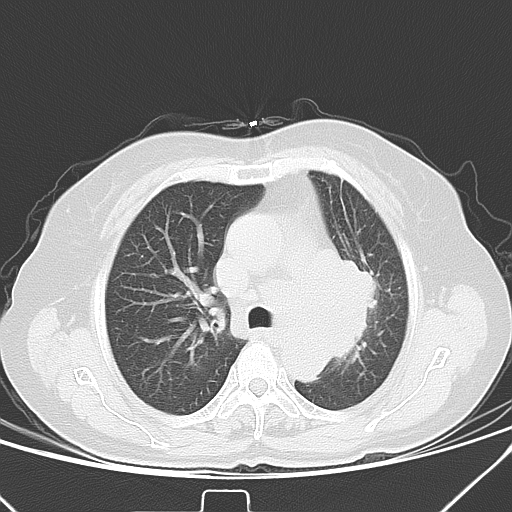
Chest CT, one axial slice; position 27 of 40 along the scan axis; 120 kVp; lung window (W 1500 / L -600 HU); 512 × 512 image matrix, field of view 331 × 331 mm. Patient: female, 59 years. Case-level facts recorded for this patient, not image findings: clinical TNM (as recorded): T3 N1 M0; histopathological grade: G3.
Structures marked on this image (bounding box drawn by a radiologist):
- lung tumour (recorded histology: small cell carcinoma): box from (x=329, y=239) to (x=376, y=371) px